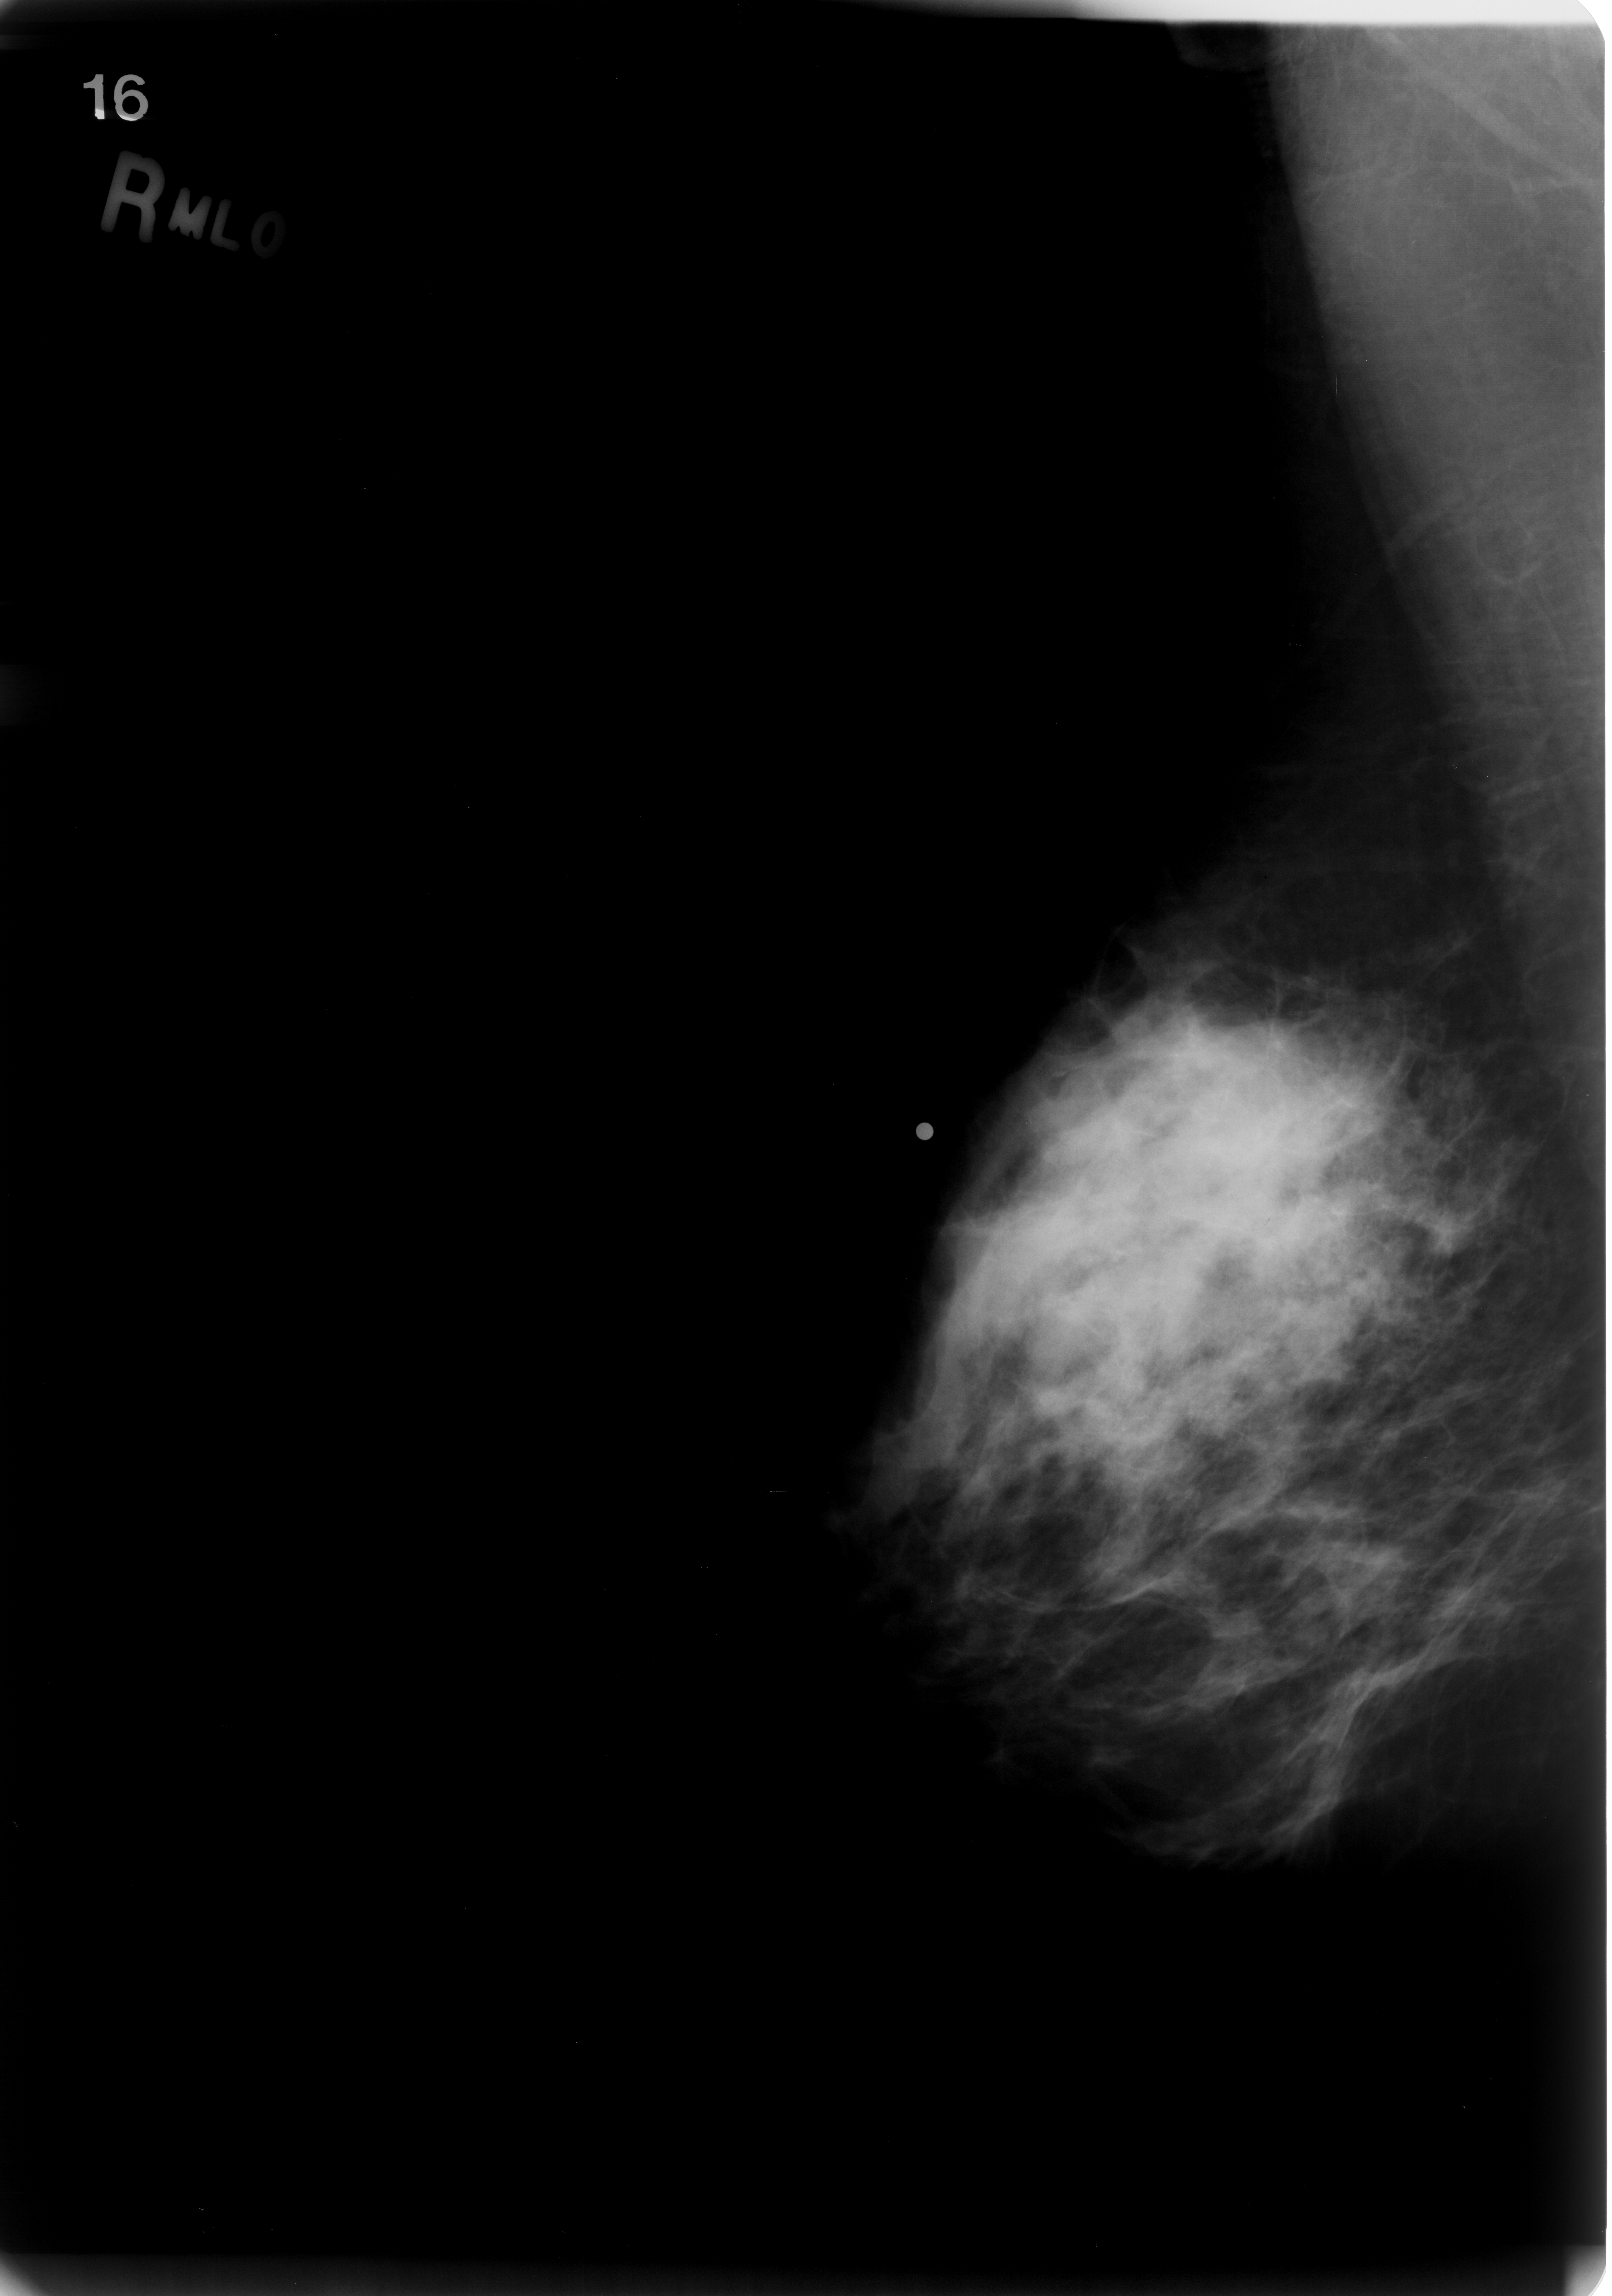
Digitized screen-film mammogram. Right breast. MLO view. Breast composition: scattered fibroglandular densities (BI-RADS density category 2 of 4). 1612 × 2296 image matrix.
Marked abnormalities (boxes around the expert regions of interest):
- mass, shape asymmetric breast tissue, margins ill defined; BI-RADS assessment category 5; pathology (as recorded): malignant: box from (x=923, y=957) to (x=1452, y=1472) px